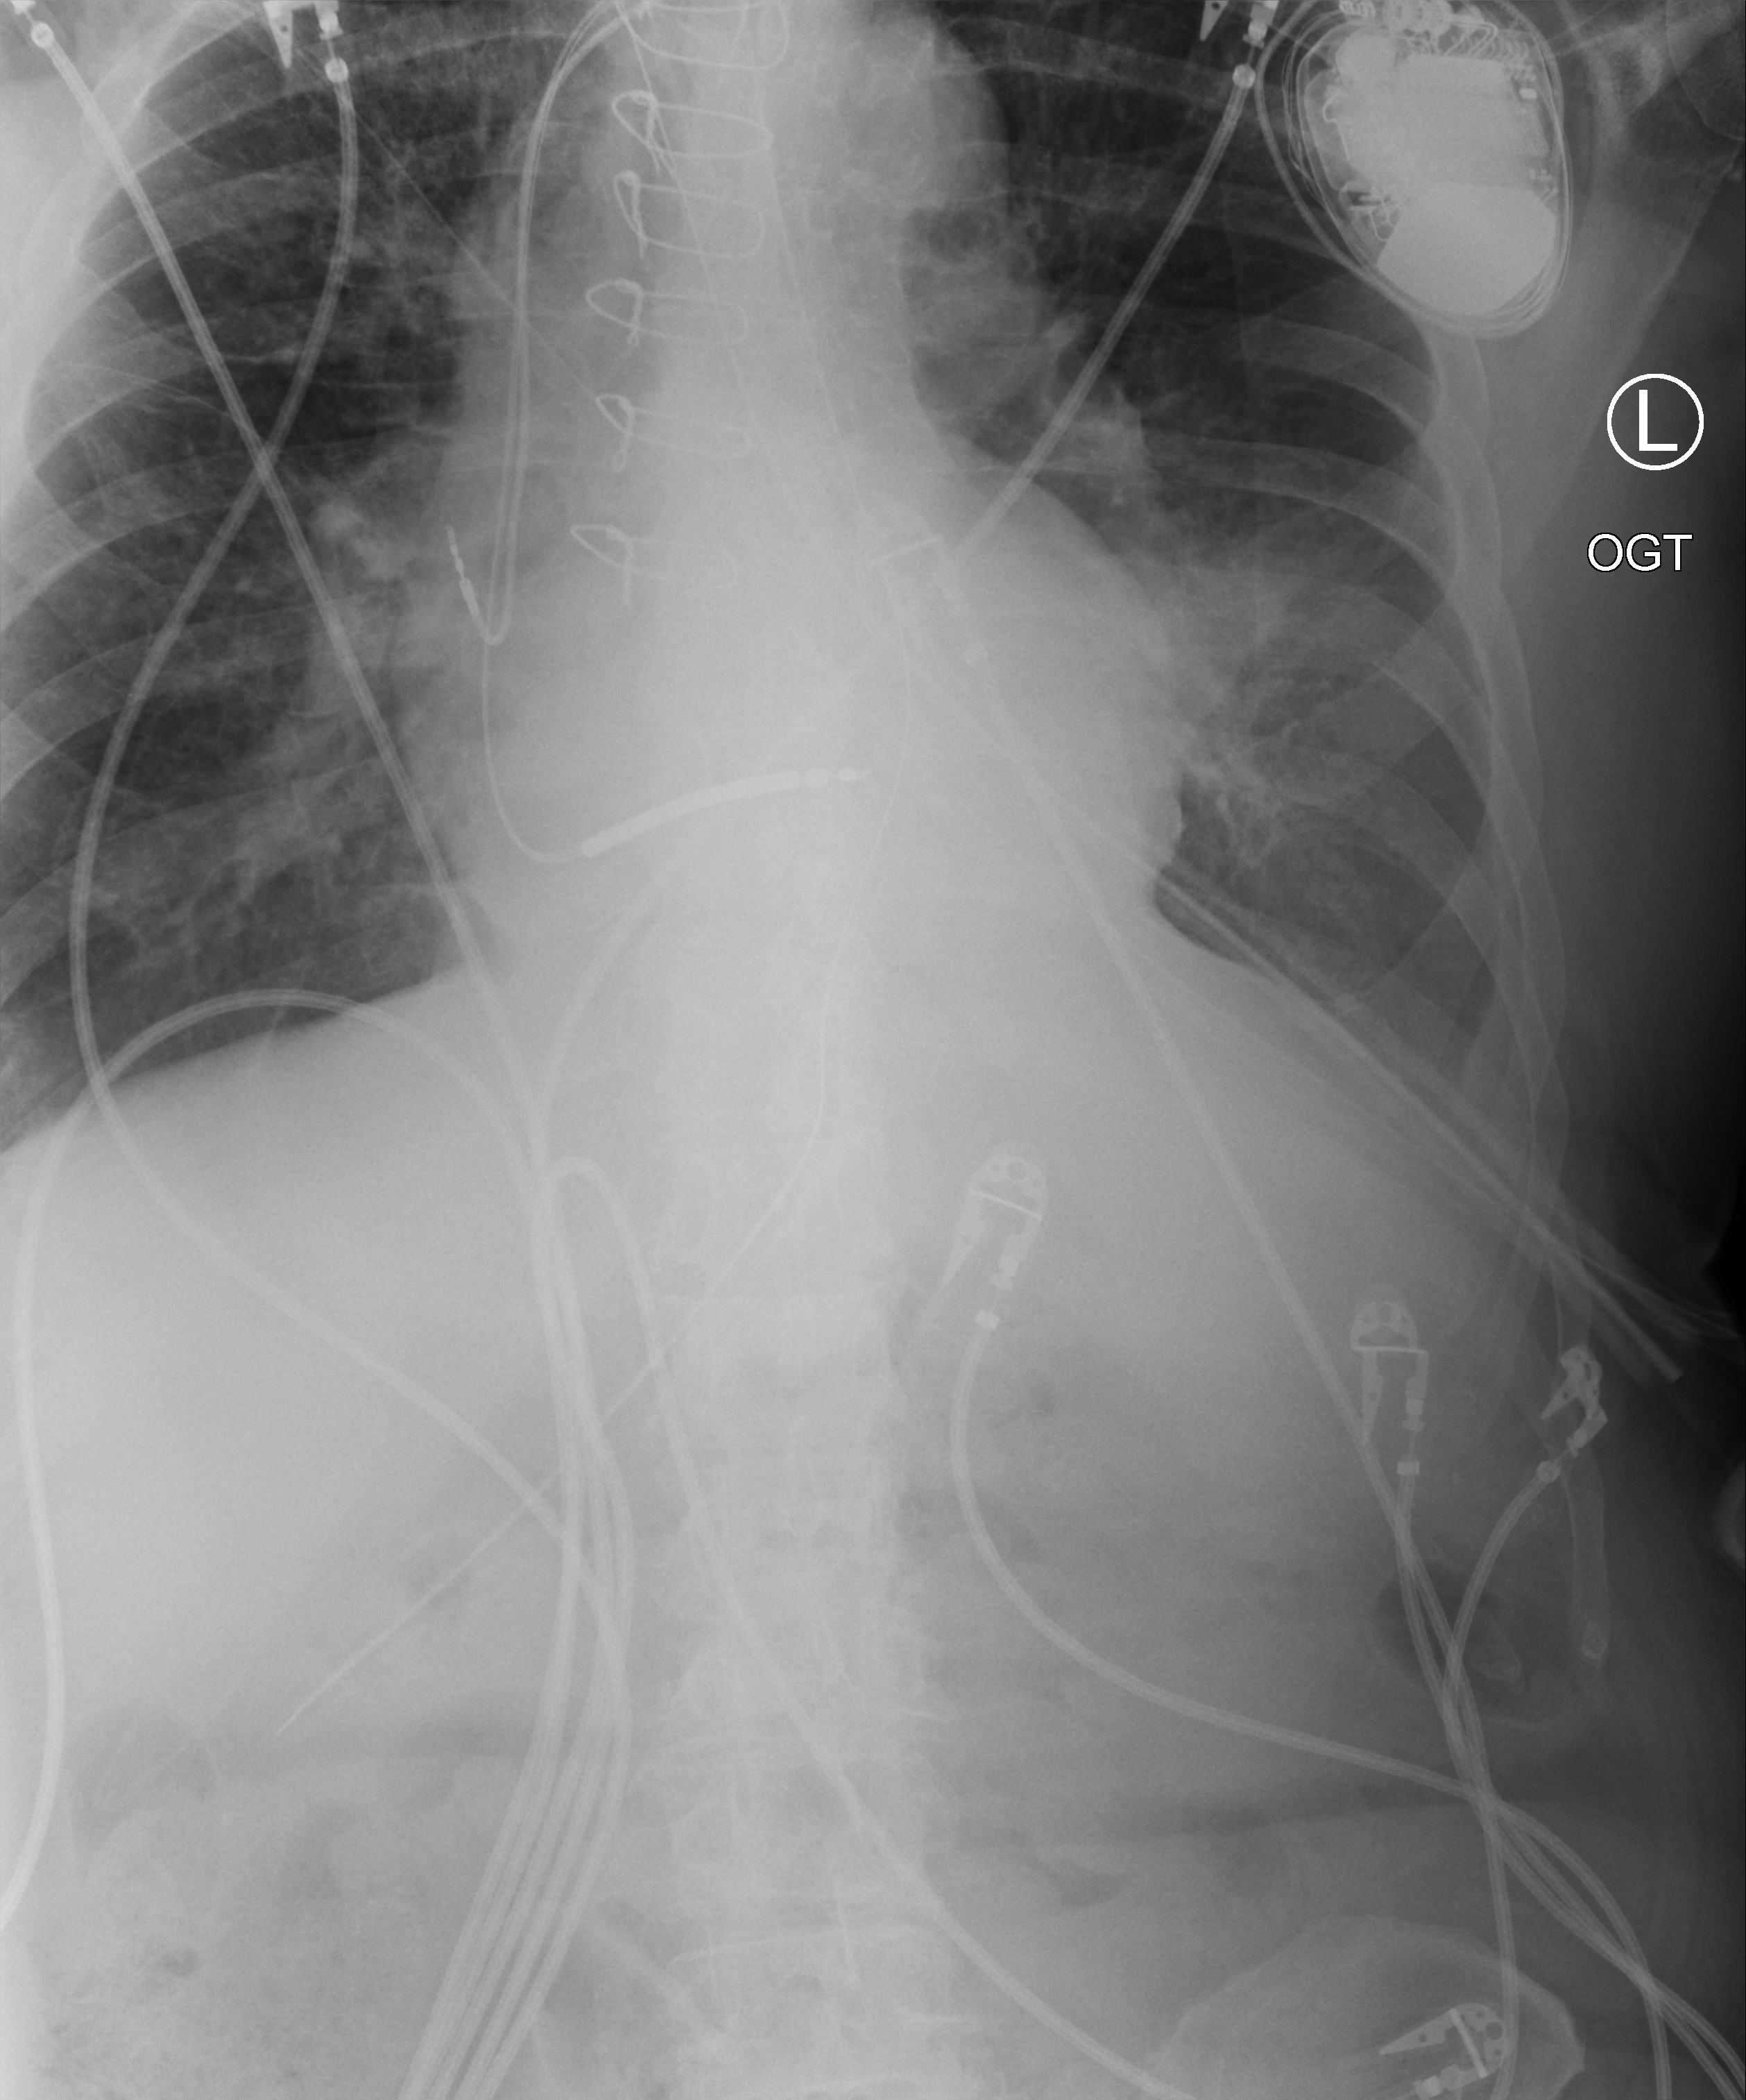
Chest X-ray (portable); anteroposterior (AP) projection. Patient hospitalised with COVID-19; male, aged 75–90 years.
From the hospital-stay record, not from the radiograph (when in the stay this image was taken is not recorded): mechanically ventilated during this hospital stay: yes.